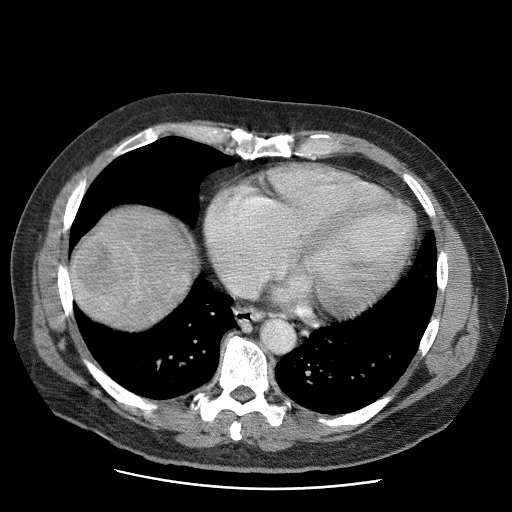
Contrast-enhanced abdominal CT (liver protocol), one axial slice. Position 62 of 81 along the scan axis. Reconstruction kernel STANDARD. 120 kVp. Soft-tissue window (W 400 / L 40 HU). 512 × 512 image matrix, field of view 380 × 380 mm. Case-level facts recorded for this patient, not image findings: diagnosis: hepatocellular carcinoma (patient treated with transarterial chemoembolisation; whether this scan precedes or follows treatment is not stated here); TNM stage (as recorded): Stage-IIIA; Child-Pugh class: A; tumour differentiation: moderately differentiated; tumour size: 5.5 cm.
Outlined on this slice (semi-automatically segmented with operator editing):
- liver parenchyma outside the tumour (the mass and vessels are separate outlines, so this box may not span the whole liver): bounding box [x1, y1, x2, y2] px = [70, 206, 196, 328]
- mass: [69, 232, 141, 322]